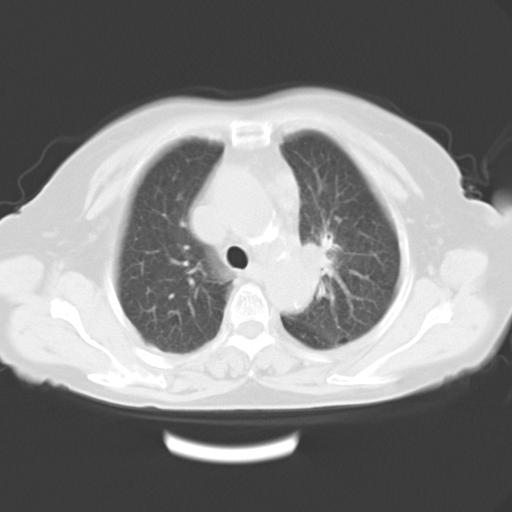
Chest CT, one axial slice; slice 20 of 26 in the series (ordered by position); reconstruction kernel B40f; lung window (W 1500 / L -600 HU); 10 mm slice thickness; 512 × 512 image matrix, field of view 353 × 353 mm. Female patient, age 71 years. From the clinical record (not read from this slice): clinical TNM (as recorded): T3 N3 M0.
Structures marked on this image (rectangle marked by the reading radiologist):
- lung tumour (recorded histology: adenocarcinoma): bounding box [x1, y1, x2, y2] px = [294, 231, 343, 289]